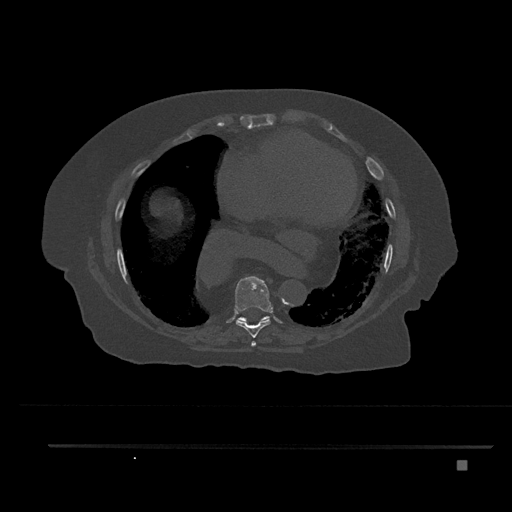
CT including the spine, one axial slice; slice 432 of 797 in the series (ordered by position); 120 kVp; bone window (W 1800 / L 400 HU); 0.5 mm slice thickness; 512 × 512 image matrix, field of view 437 × 437 mm. Patient: female, 76 years. Case-level facts recorded for this patient, not image findings: primary cancer: lung; vertebrae with lytic lesions (as recorded): T11, L3.
Structures marked on this image (semi-automatic segmentation, software-assisted and operator-edited):
- T7 vertebra: box from (x=251, y=341) to (x=256, y=346) px
- T8 vertebra: (x=235, y=276)–(x=271, y=347)
- T9 vertebra: (x=238, y=316)–(x=270, y=322)